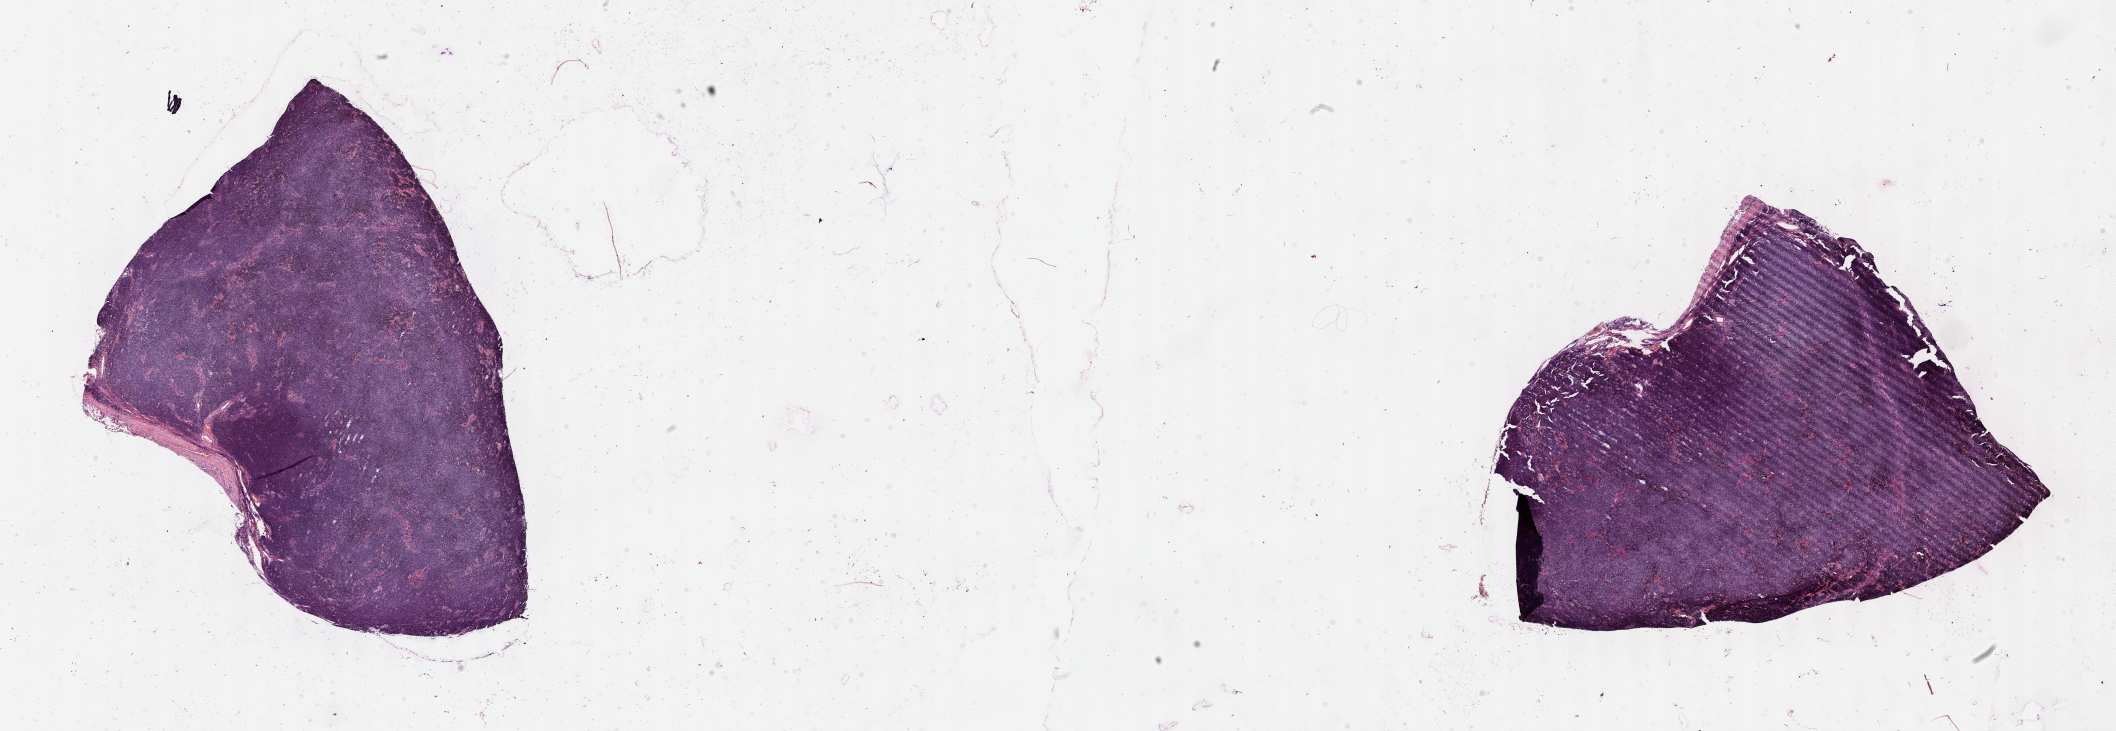
Hematoxylin and eosin (H&E) stained whole-slide image, low-resolution overview of the scanned area, about 34.2 x 11.8 mm, FFPE section, metastatic tumour sample, sampled site: lymph nodes of axilla or arm. Female, age 54 years at initial diagnosis.
This section: metastatic tumour tissue. Patient diagnosis: Malignant melanoma, NOS.